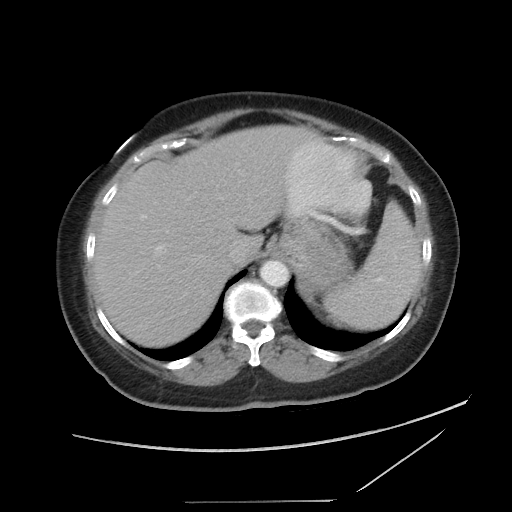
Contrast-enhanced abdominal CT, one axial slice. Position 67 of 86 along the scan axis. 120 kVp. Intravenous contrast given. Soft-tissue window (W 400 / L 40 HU). 512 × 512 image matrix, field of view 398 × 398 mm. Female patient, age 77 years. From the clinical record (not read from this slice): diagnosis: adrenocortical carcinoma; tumour side: left adrenal; tumour size at pathology: 13.1 cm; Ki-67 index: 10 %; stage (as recorded): 3.
Annotated regions visible in this slice (semi-automatic segmentation, software-assisted and operator-edited):
- mass: bounding box [x1, y1, x2, y2] px = [289, 222, 353, 288]